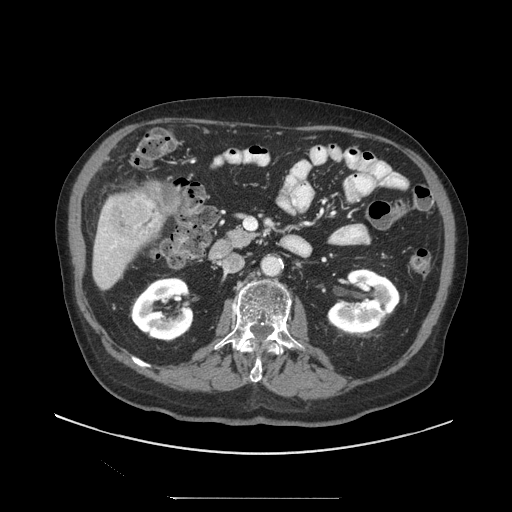
Contrast-enhanced abdominal CT (liver protocol), one axial slice; slice 34 of 97 in the series (ordered by position); reconstruction kernel STANDARD; soft-tissue window (W 400 / L 40 HU); 2.5 mm slice thickness; 512 × 512 image matrix, field of view 450 × 450 mm. Case-level facts recorded for this patient, not image findings: diagnosis: hepatocellular carcinoma (patient treated with transarterial chemoembolisation; whether this scan precedes or follows treatment is not stated here); TNM stage (as recorded): Stage-IIIC; Child-Pugh class: A; tumour differentiation: well differentiated; tumour size: 9.2 cm.
Annotated regions visible in this slice (semi-automatically segmented with operator editing):
- liver parenchyma outside the tumour (the mass and vessels are separate outlines, so this box may not span the whole liver): bounding box [x1, y1, x2, y2] px = [92, 186, 162, 290]
- mass: [110, 190, 162, 240]
- liver vessels: [102, 229, 117, 248]